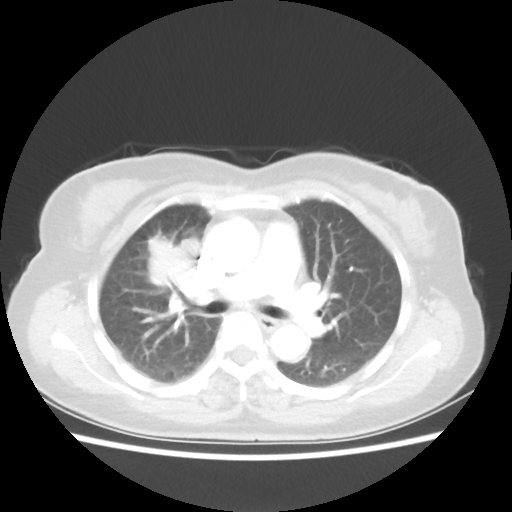
Chest CT, one axial slice; slice 33 of 55 in the series (ordered by position); reconstruction kernel STANDARD; 80 kVp; lung window (W 1500 / L -600 HU); 5 mm slice thickness; 512 × 512 image matrix, field of view 337 × 337 mm. Female patient, age 62 years. Case-level facts recorded for this patient, not image findings: clinical TNM (as recorded): T4 N3 M0.
Outlined on this slice (rectangle marked by the reading radiologist):
- lung tumour (recorded histology: squamous cell carcinoma): bounding box <129,221,204,310> (left, top, right, bottom; pixels)